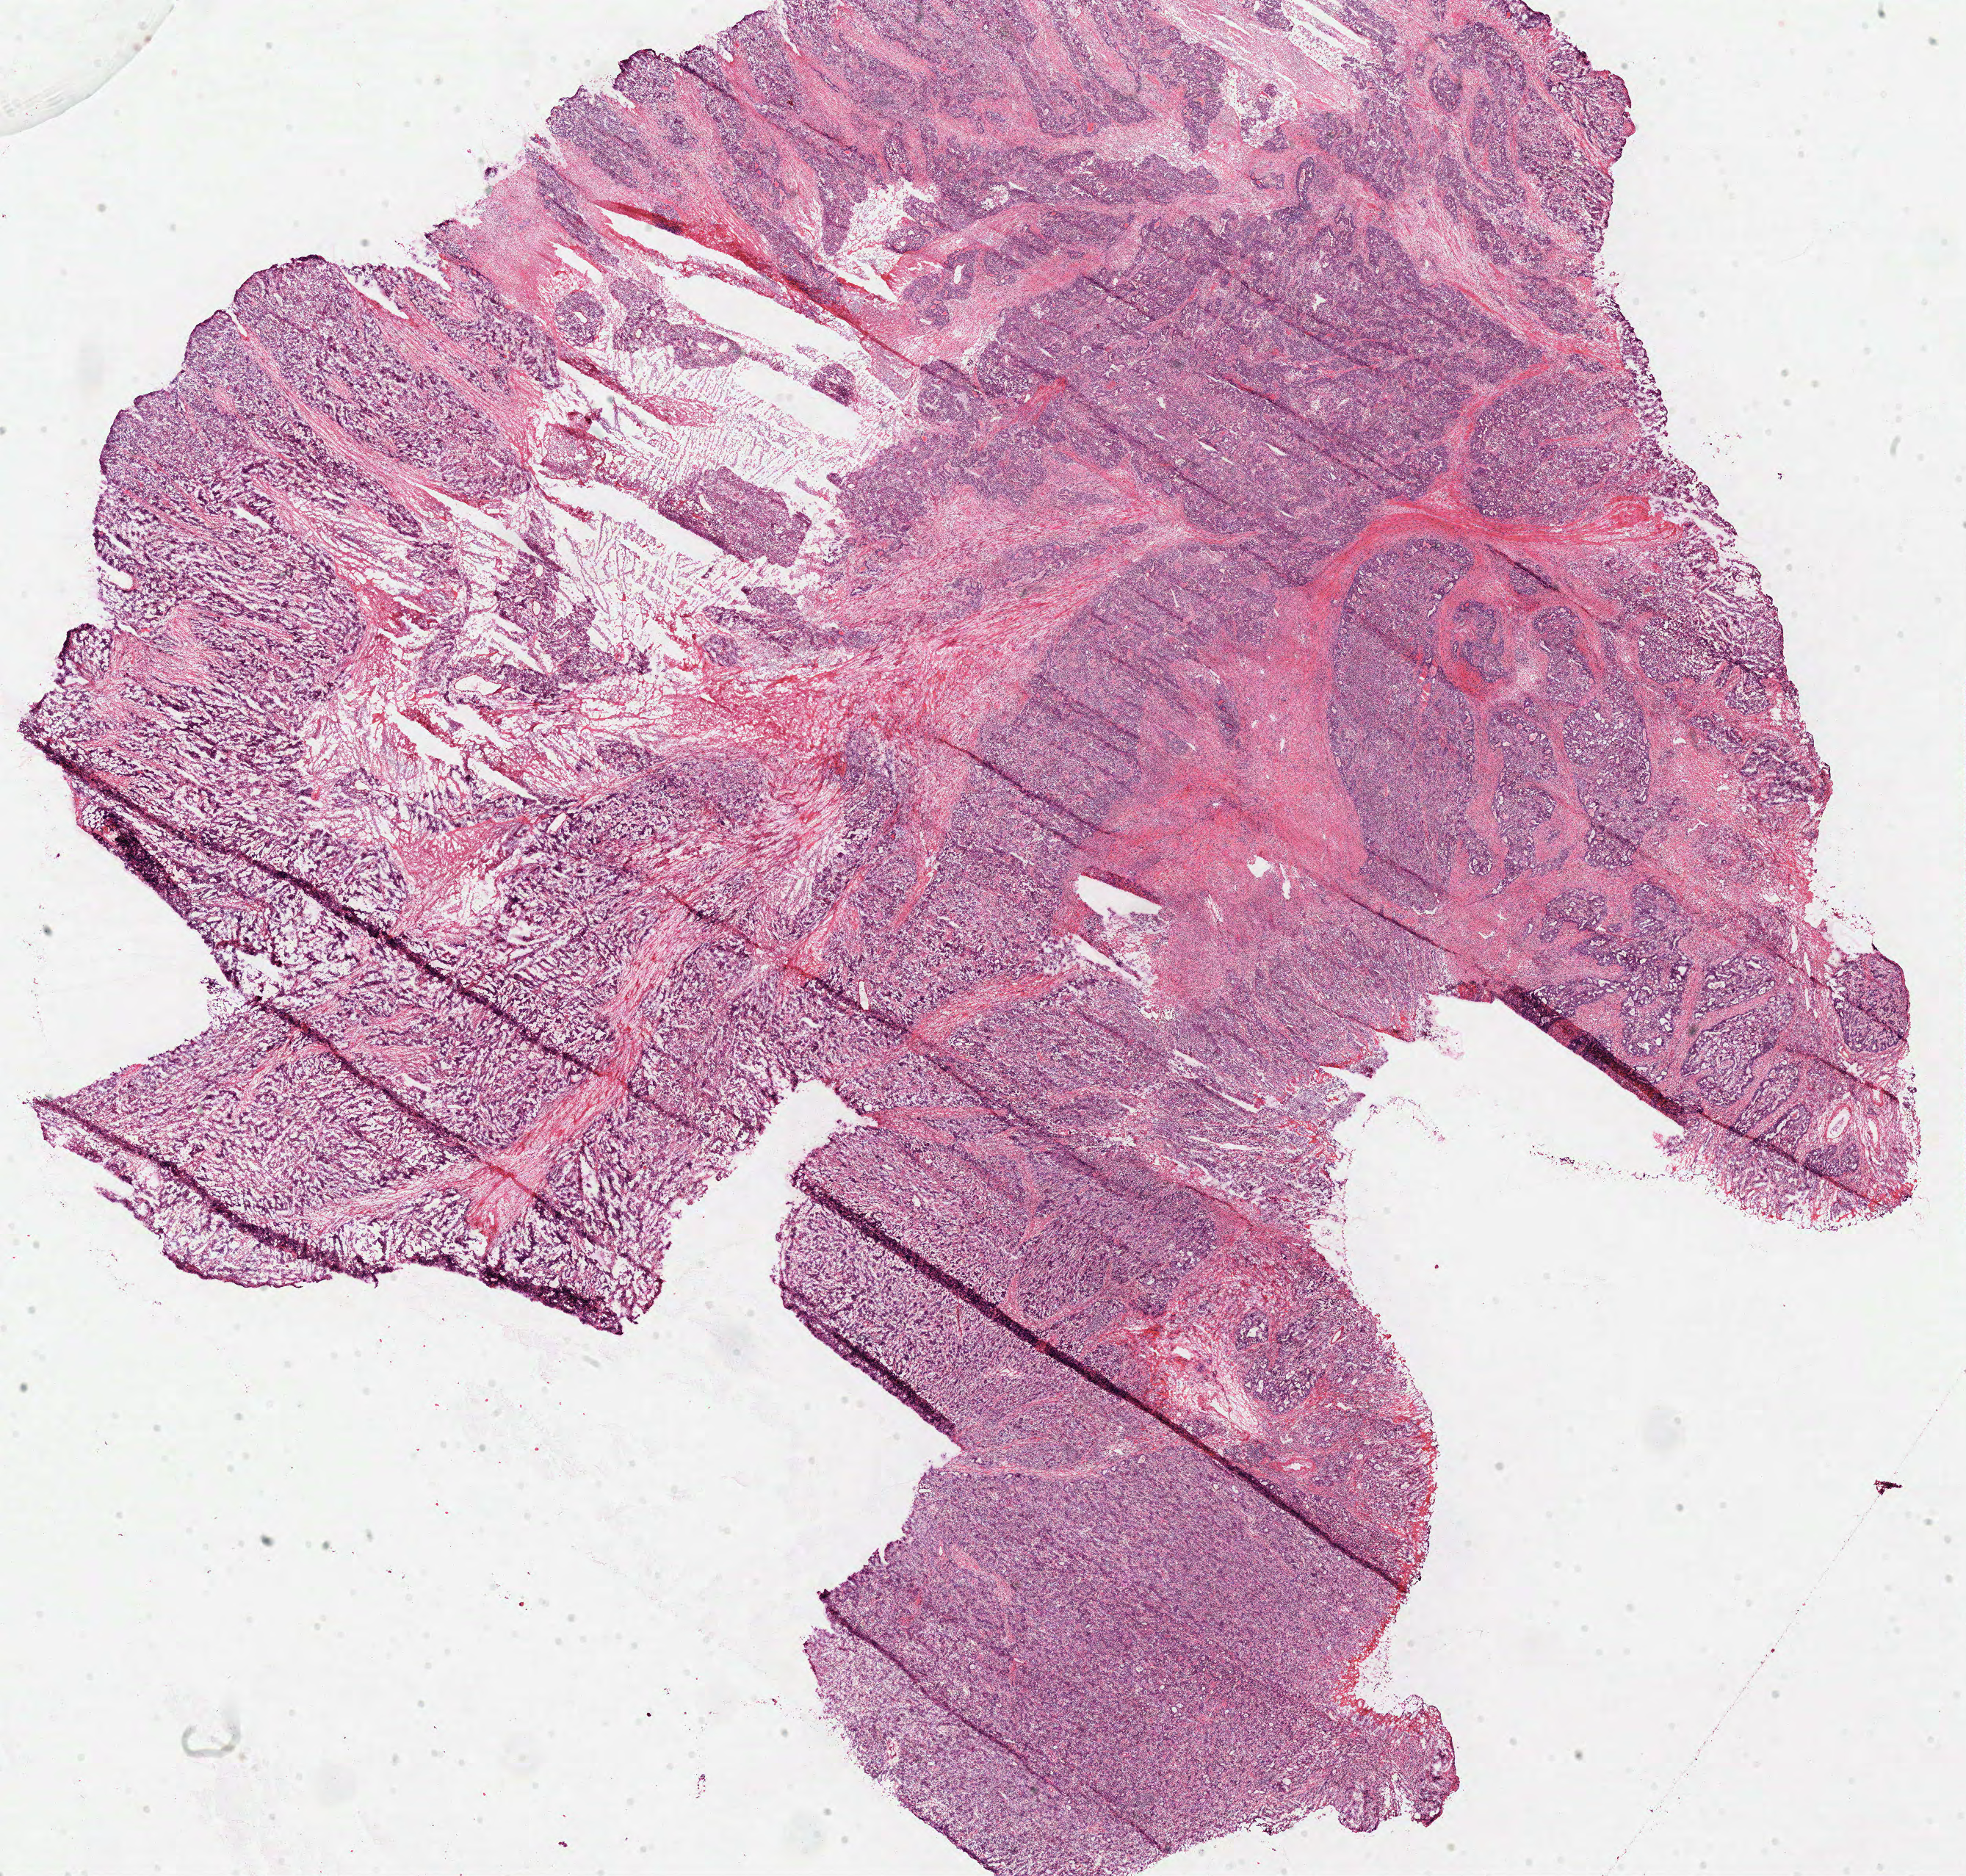
Whole-slide histology image, H&E-stained, a low-resolution overview of the entire scanned area, about 21.1 x 20.1 mm. Frozen section from the top of the tissue portion. Sample: primary tumour, stomach. Patient: male, age at initial diagnosis 75 years. Histologic grade: G3 (poorly differentiated). Pathologist review of this section (percent, as recorded): tumour cells 70%, tumour nuclei 80%, normal cells 0%, stromal cells 15%, necrosis 15%.
* diagnosis: Adenocarcinoma, NOS (body of stomach)
* TNM: T3 N0 M0
* AJCC pathologic stage: IIA (7th edition)
* lymph nodes positive (case pathology): 0 of 15 examined